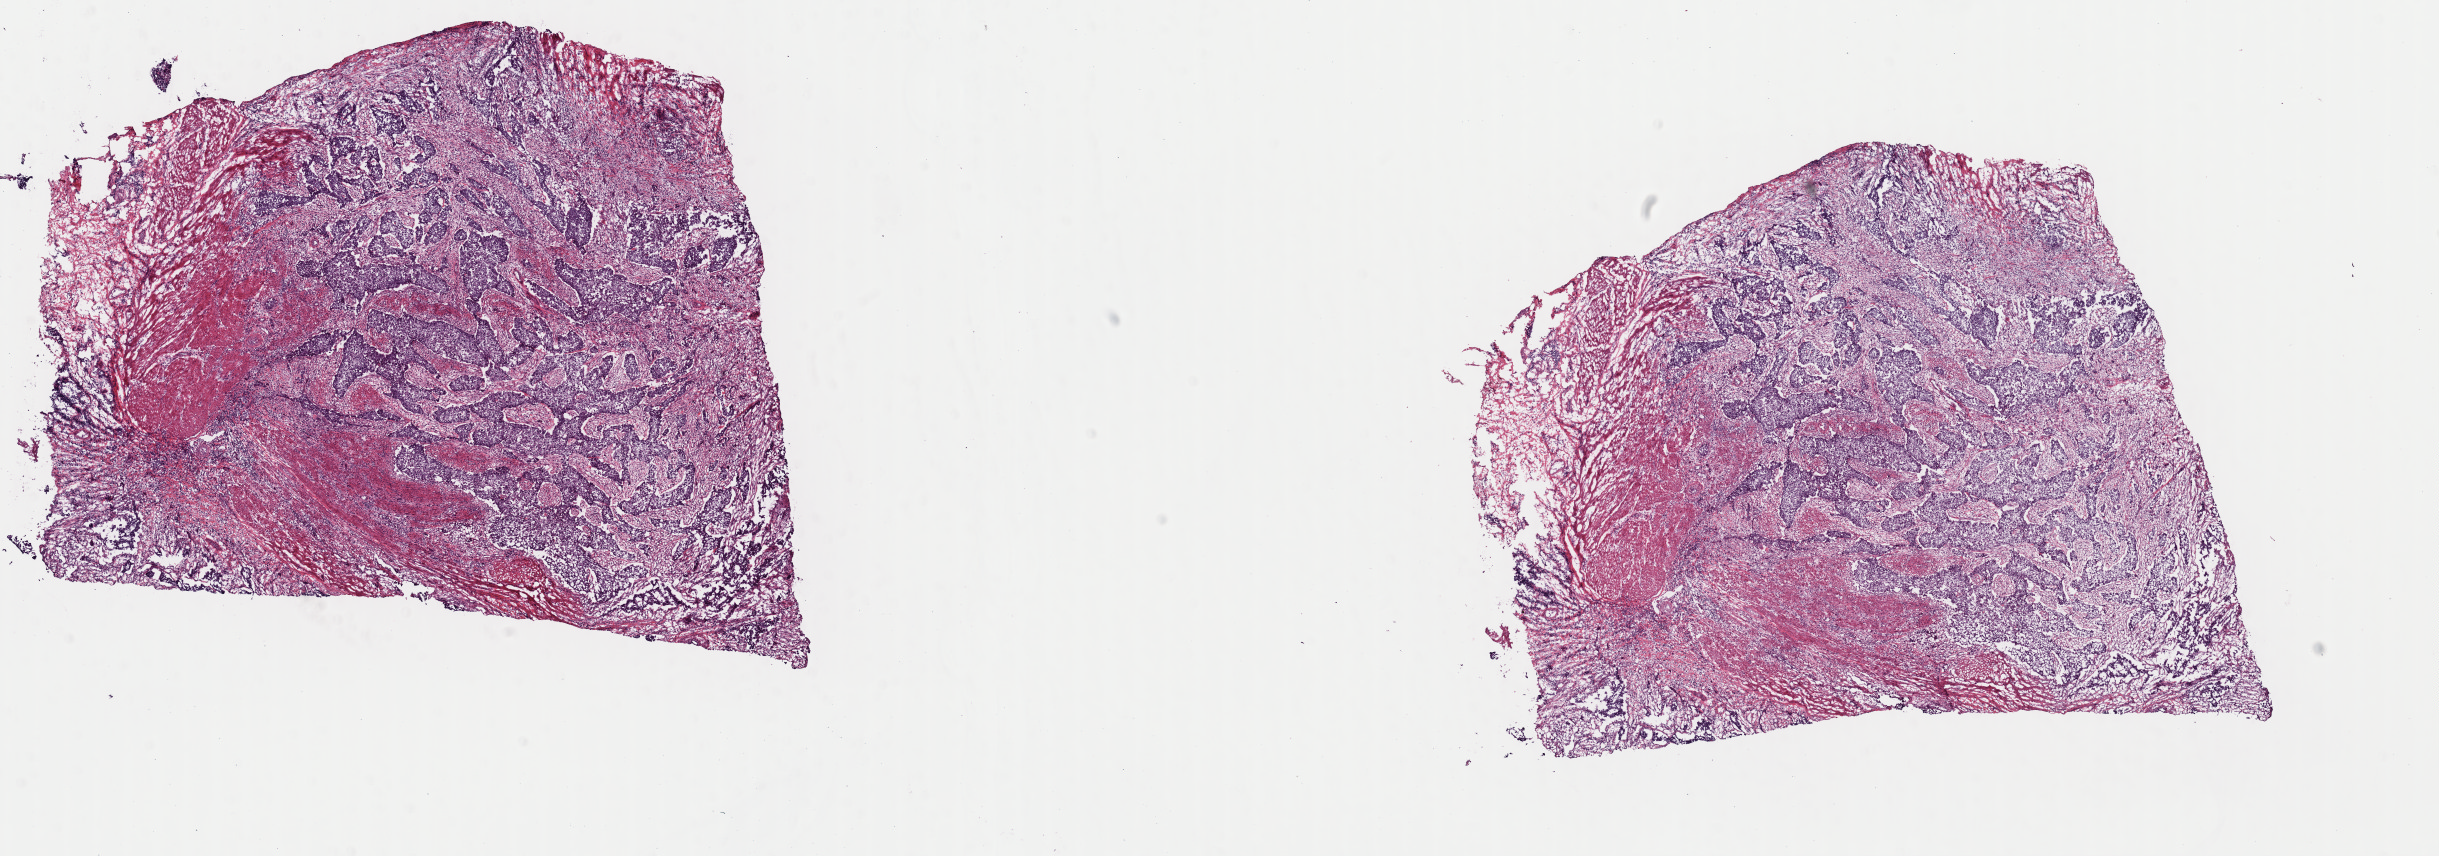
Whole-slide histology image, H&E, whole scanned area (about 19.3 x 6.8 mm) shown as a low-resolution overview, frozen section, primary tumour sample from the bladder. Patient: male, age at initial diagnosis 66 years. Histologic grade: high grade. Slide review estimates, as recorded: tumour cells 45%, tumour nuclei 70%, normal cells 0%, stromal cells 54%, necrosis 1%. Infiltration values recorded for this section: lymphocyte infiltration 1%, monocyte infiltration 0%, neutrophil infiltration 0%.
• AJCC pathologic stage: III (7th edition)
• lymph nodes positive (case pathology): 0 of 6 examined
• TNM: T3a N0 MX
• pathologic diagnosis: Transitional cell carcinoma